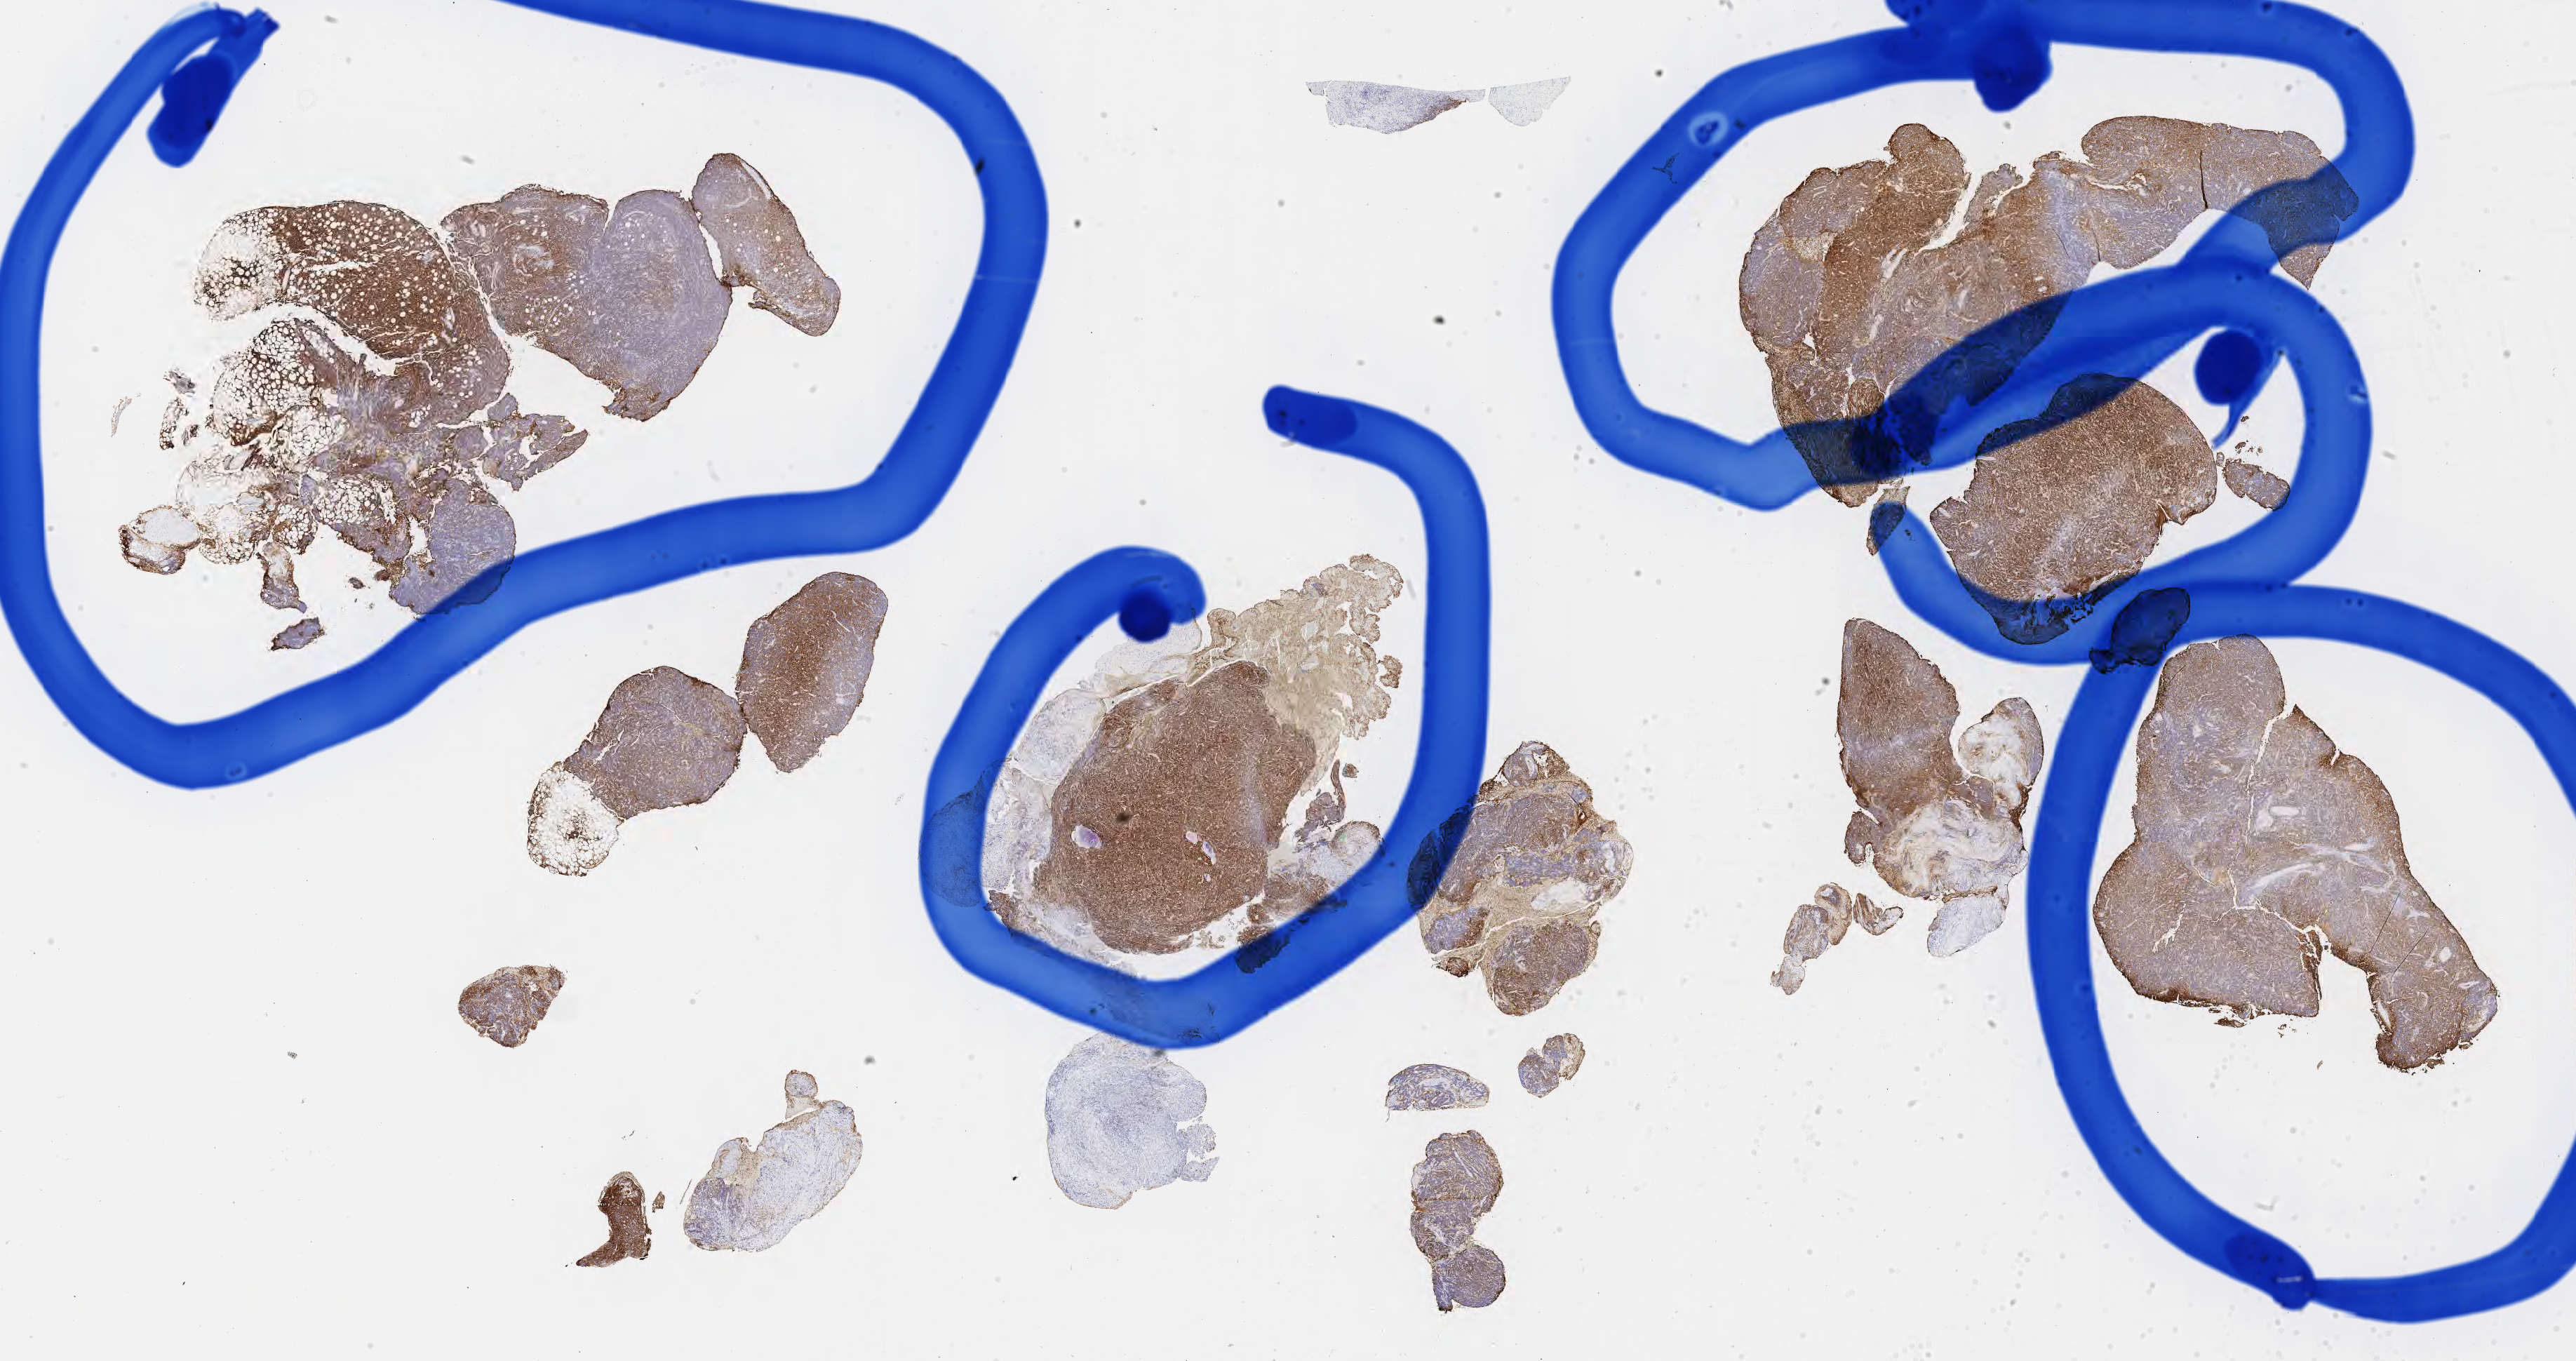
IHC for CD20, whole-slide image — a low-resolution overview of the entire scanned area, about 29.7 x 15.7 mm. Specimen: tumor tissue. Patient: male, 45 years old.
Histologic diagnosis: Diffuse large B-cell lymphoma, NOS.